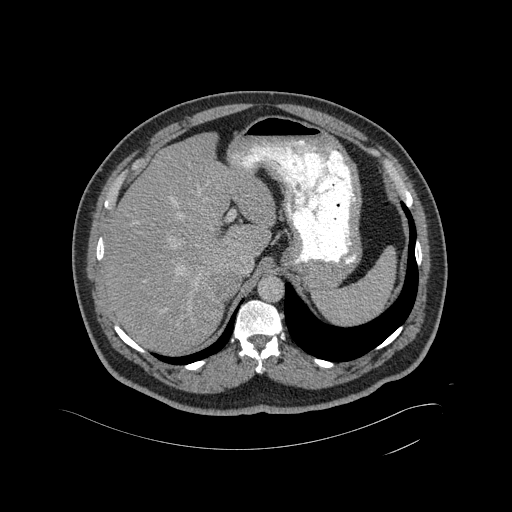
Contrast-enhanced abdominal CT, one axial slice; position 346 of 433 along the scan axis; 120 kVp; intravenous contrast given; soft-tissue window (W 400 / L 40 HU); 2 mm slice thickness; 512 × 512 image matrix, field of view 500 × 500 mm. Male patient, age 56 years. From the clinical record (not read from this slice): diagnosis: adrenocortical carcinoma; tumour side: right adrenal.
Structures marked on this image (semi-automatically segmented with operator editing):
- mass: box from (x=217, y=274) to (x=238, y=299) px